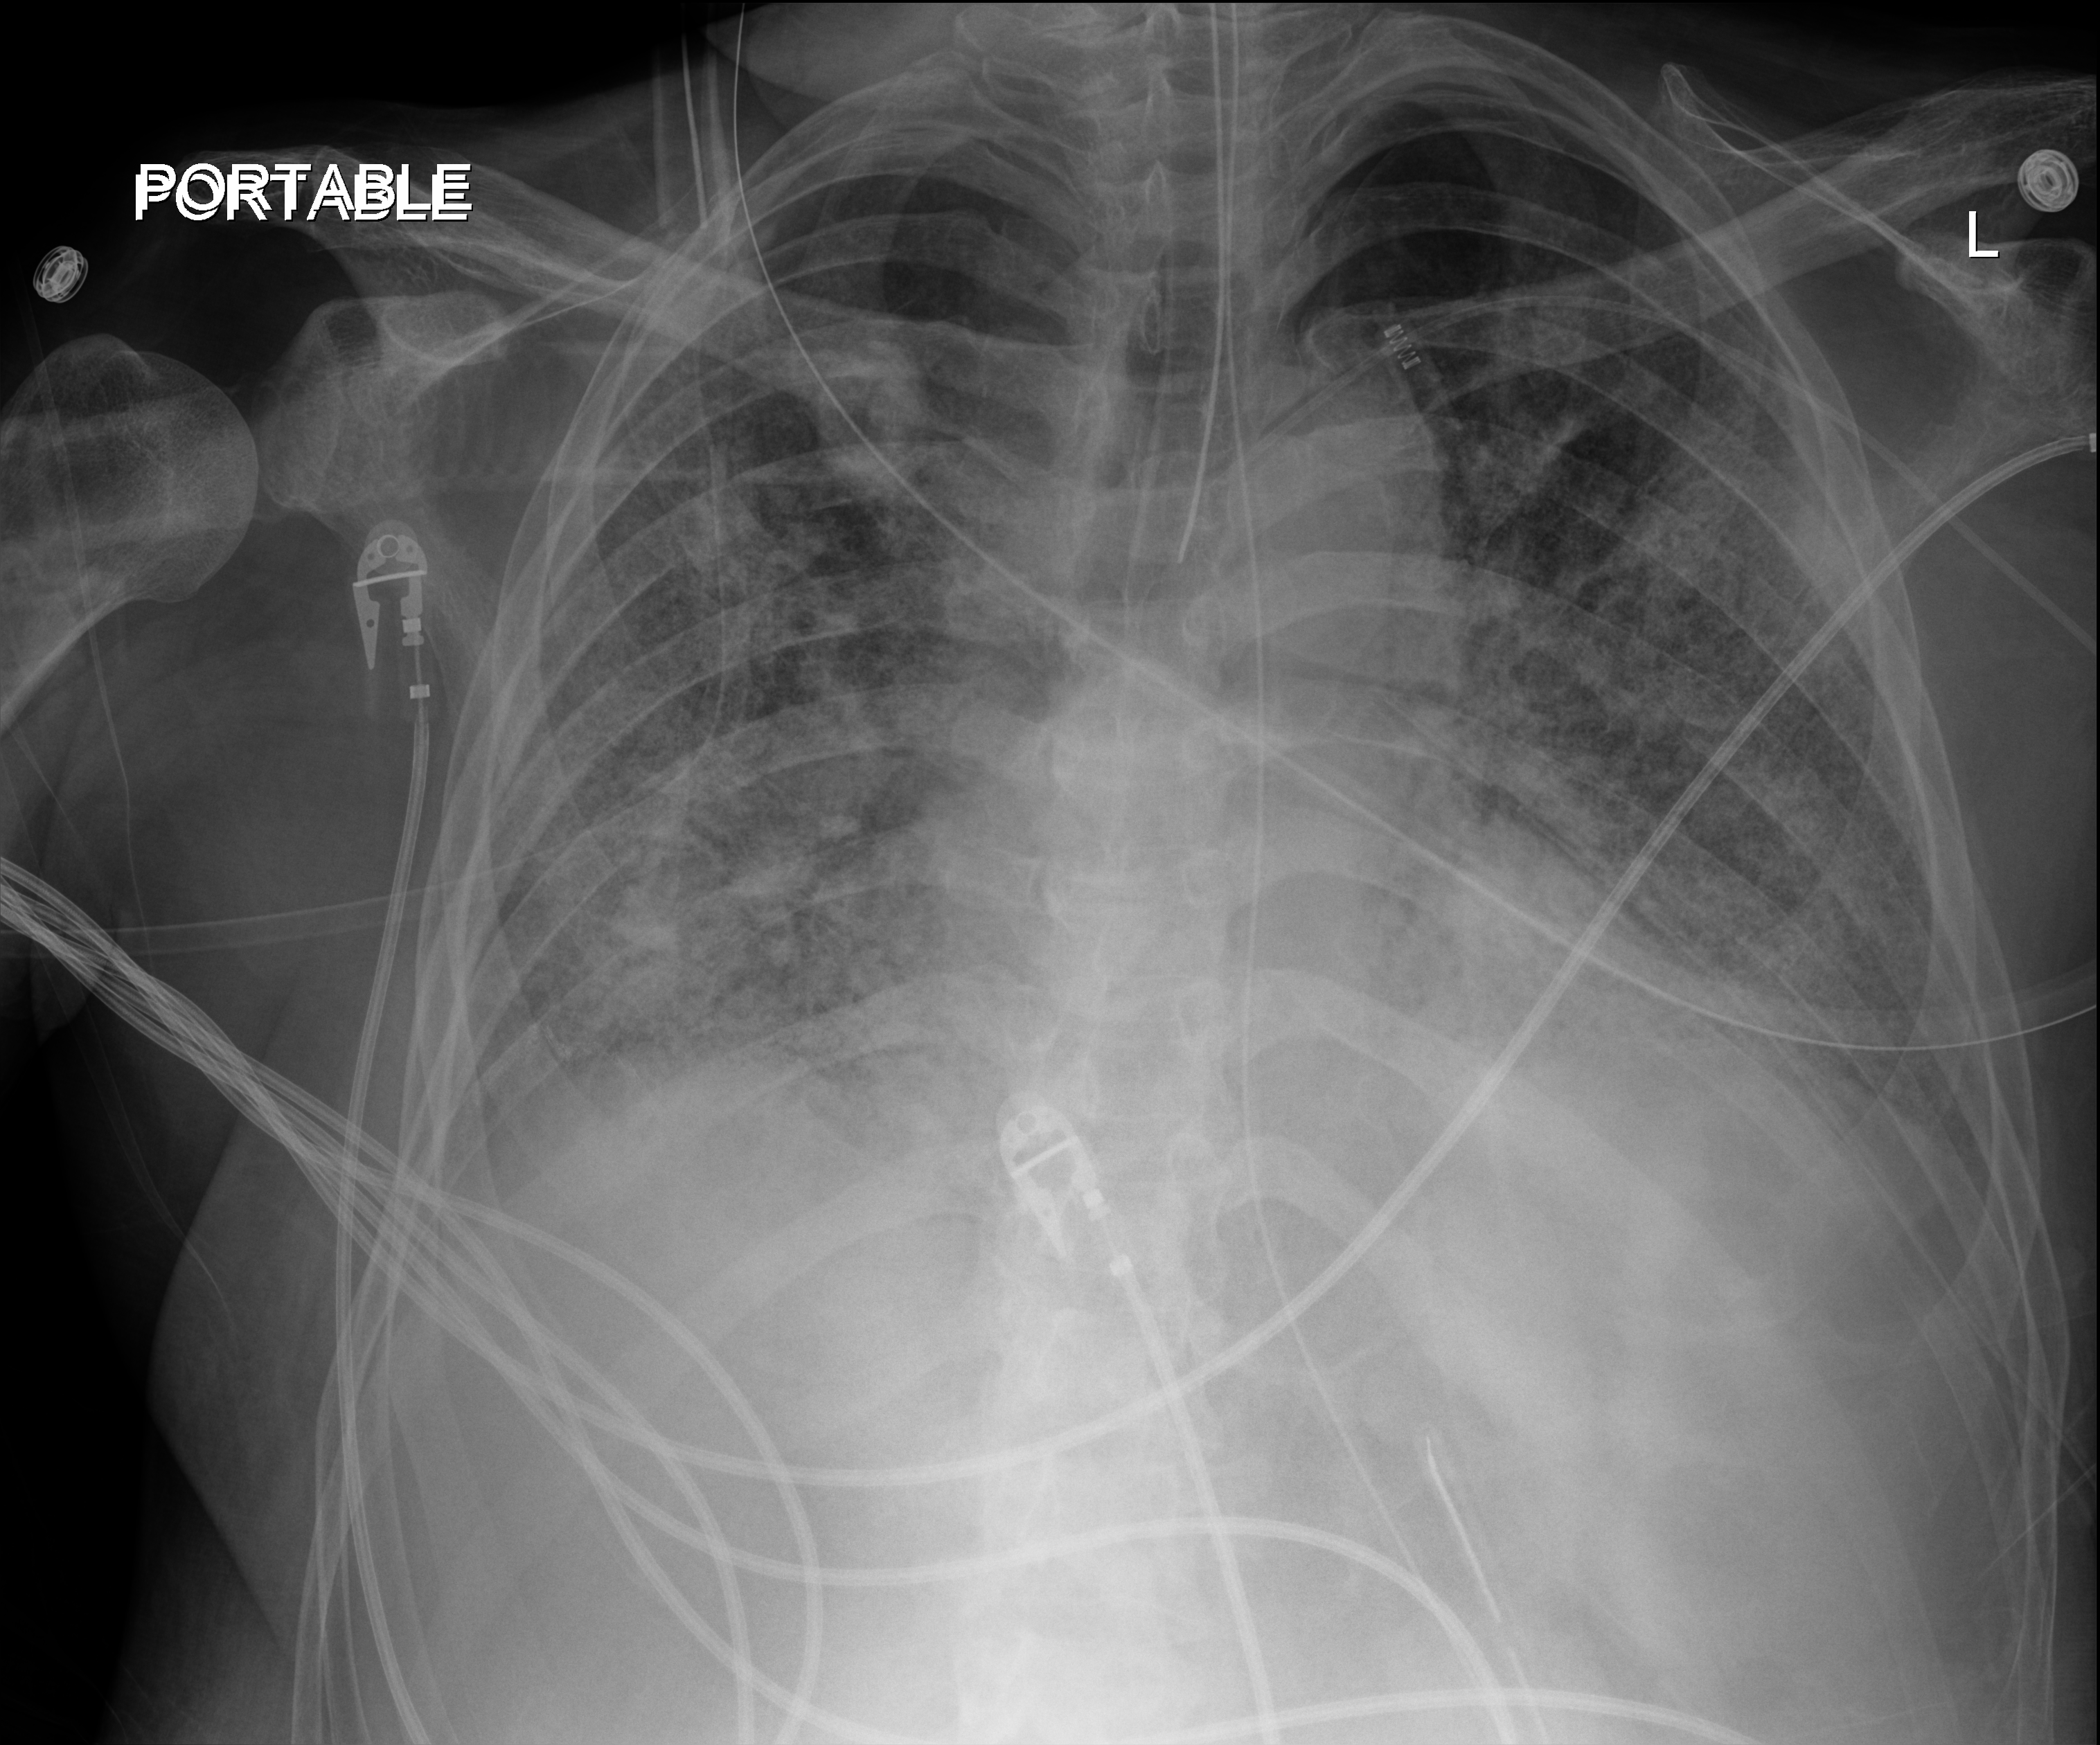
Bedside chest radiograph (digital radiography), anteroposterior (AP) projection. Patient hospitalised with COVID-19; male, aged 60–74 years.
Admission-level facts for this patient (not findings on this image; timing relative to this image not recorded):
- admitted to intensive care during this hospital stay: yes
- mechanically ventilated during this hospital stay: yes